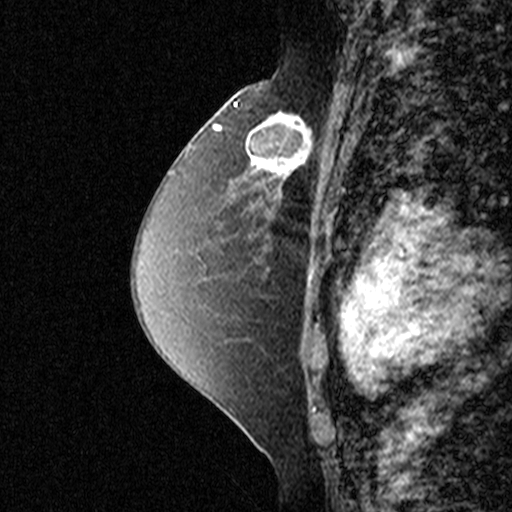
Breast MRI (dynamic contrast-enhanced), one sagittal slice; position 26 of 44 along the scan axis; dynamic contrast-enhanced study with each time point stored as its own series, time point 2 of 3 at this slice position (early post-contrast, ordered by acquisition time); 1.5 T; TE 4.5 ms, TR 11 ms; 3 mm slice thickness; 512 × 512 image matrix, field of view 200 × 200 mm. Female patient, age 49 years. From the clinical record (not read from this slice): setting: breast cancer imaged before/during neoadjuvant chemotherapy; receptor status: triple-negative.
Annotated regions visible in this slice (semi-automatically segmented with operator editing):
- analysis volume of interest (the breast-tissue region the enhancement analysis was run in; not a lesion): bounding box (x1, y1, x2, y2) in pixels: (244, 100, 335, 197)
- tumour enhancement mask (voxels above the 90 % enhancement threshold inside the analysis volume of interest): (252, 111, 313, 197)